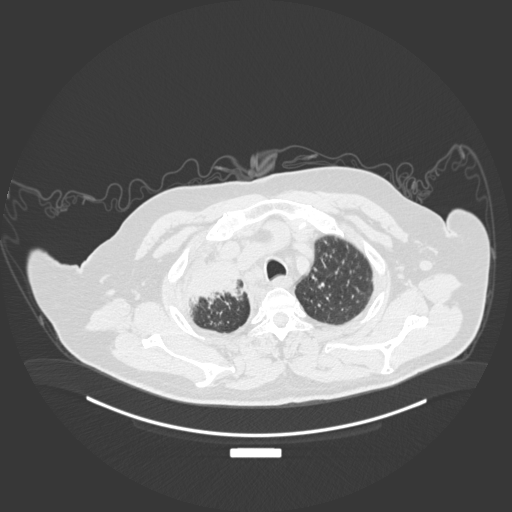
Chest CT, one axial slice; slice 163 of 201 in the series (ordered by position); 120 kVp; lung window (W 1500 / L -600 HU); 1 mm slice thickness; 512 × 512 image matrix, field of view 500 × 500 mm. Male patient, age 69 years. Case-level facts recorded for this patient, not image findings: clinical TNM (as recorded): T4 N3 M1.
Annotated regions visible in this slice (rectangle marked by the reading radiologist):
- lung tumour (recorded histology: adenocarcinoma): bounding box <180,250,249,314> (left, top, right, bottom; pixels)